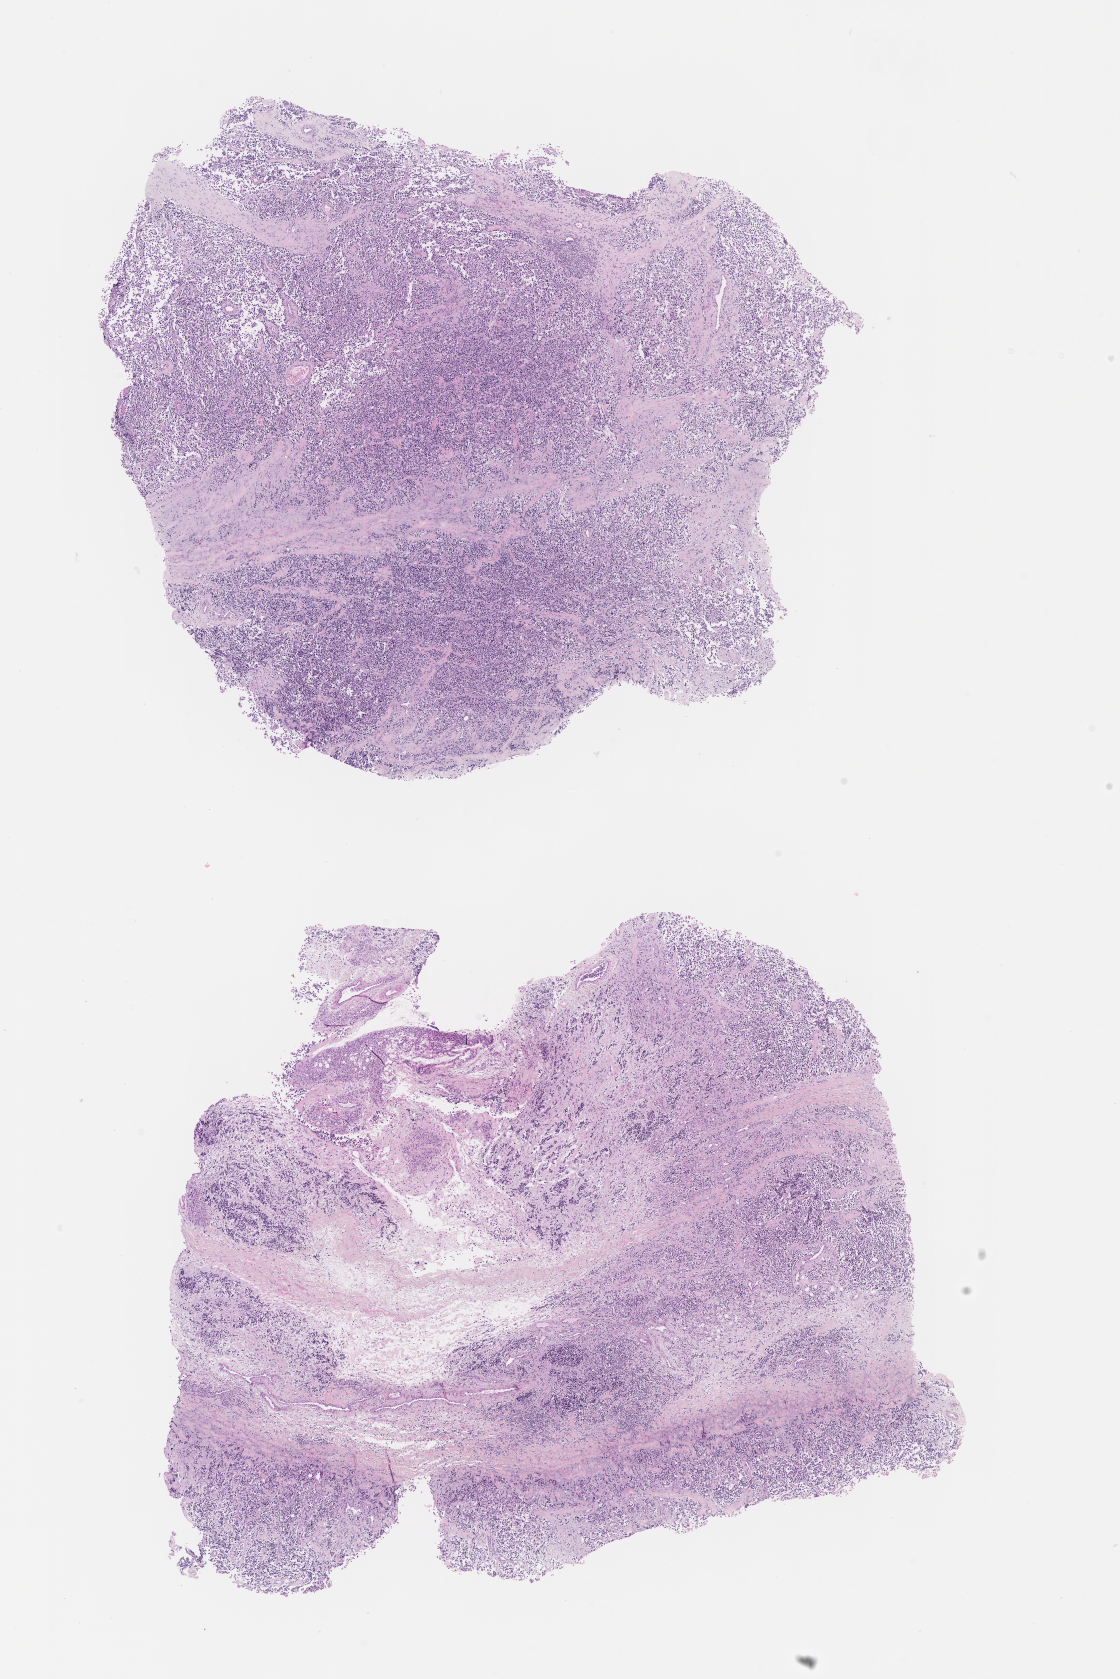
Digitized hematoxylin and eosin (H&E)-stained section of tumor tissue, whole scanned area (about 9.1 x 13.6 mm) shown as a low-resolution overview. Formalin-fixed paraffin-embedded section. Sample anatomic site: soft tissue, leg. Patient: male, age 12.5 years at diagnosis.
Diagnosis: rhabdomyosarcoma; histological classification: alveolar rhabdomyosarcoma. Stage (as recorded): 4.